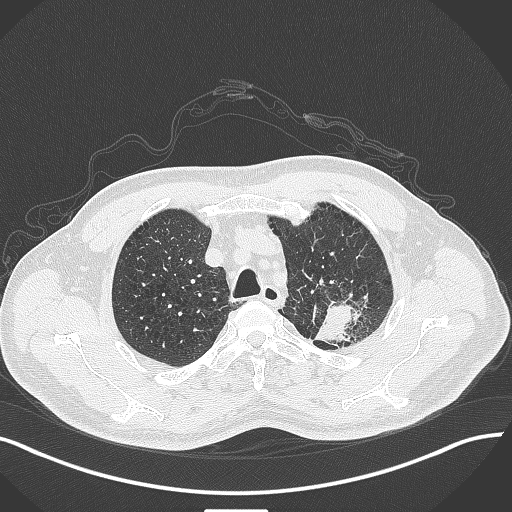
Chest CT, one axial slice. Slice 346 of 429 in the series (ordered by position). Reconstruction kernel B70f. 120 kVp. Lung window (W 1500 / L -600 HU). 1 mm slice thickness. 512 × 512 image matrix. Male patient, age 55 years. From the clinical record (not read from this slice): clinical TNM (as recorded): T3 N0 M1c; histopathological grade: G3.
Annotated regions visible in this slice (bounding box drawn by a radiologist):
- lung tumour (recorded histology: adenocarcinoma): bounding box (x1, y1, x2, y2) in pixels: (310, 294, 368, 351)